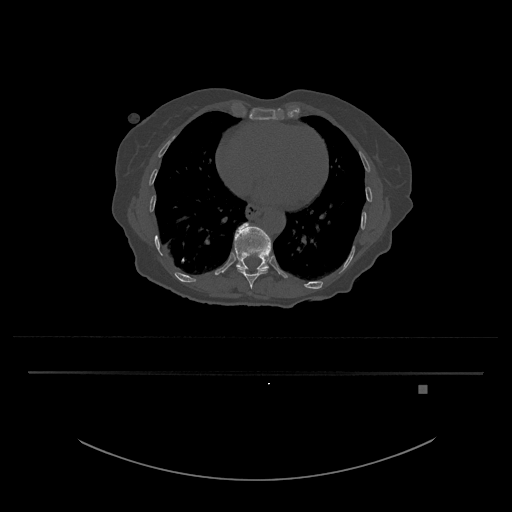
CT including the spine, one axial slice. Position 692 of 797 along the scan axis. Reconstruction kernel Br40s/3. Bone window (W 1800 / L 400 HU). 0.5 mm slice thickness. 512 × 512 image matrix, field of view 500 × 500 mm. Patient: female, 57 years. From the clinical record (not read from this slice): primary cancer: cervical.
Annotated regions visible in this slice (semi-automatic segmentation, software-assisted and operator-edited):
- T10 vertebra: bounding box <238,269,268,289> (left, top, right, bottom; pixels)
- T11 vertebra: <234,223,272,270>